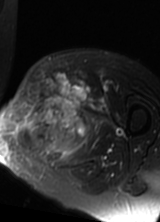
MRI of an extremity soft-tissue mass, one axial slice; slice 42 of 69 in the series (ordered by position); T2-weighted fat-saturated; MR volume resampled by the dataset authors to the PET/CT grid (not the native acquisition matrix); 160 × 222 image matrix. Female patient. From the clinical record (not read from this slice): histological type: pleomorphic leiomyosarcoma; grade: high; site of the primary tumour: left thigh.
Annotated regions visible in this slice (expert contour drawn on MRI and transferred to this co-registered scan by the dataset authors):
- gross tumour volume including surrounding oedema: box from (x=18, y=72) to (x=97, y=160) px
- gross tumour volume (mass): (x=32, y=72)–(x=87, y=149)